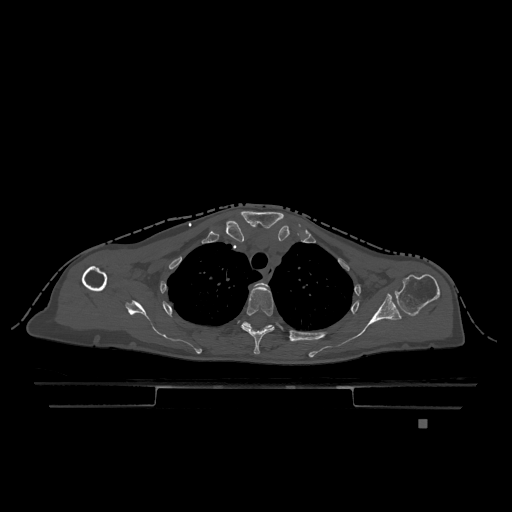
CT including the spine, one axial slice. Position 916 of 1317 along the scan axis. Bone window (W 1800 / L 400 HU). 0.5 mm slice thickness. 512 × 512 image matrix. Female patient, age 74 years. From the clinical record (not read from this slice): primary cancer: lung.
Outlined on this slice (semi-automatically segmented with operator editing):
- T2 vertebra: bounding box (x1, y1, x2, y2) in pixels: (254, 282, 267, 288)
- T3 vertebra: (241, 286, 275, 354)
- T4 vertebra: (243, 322, 307, 342)